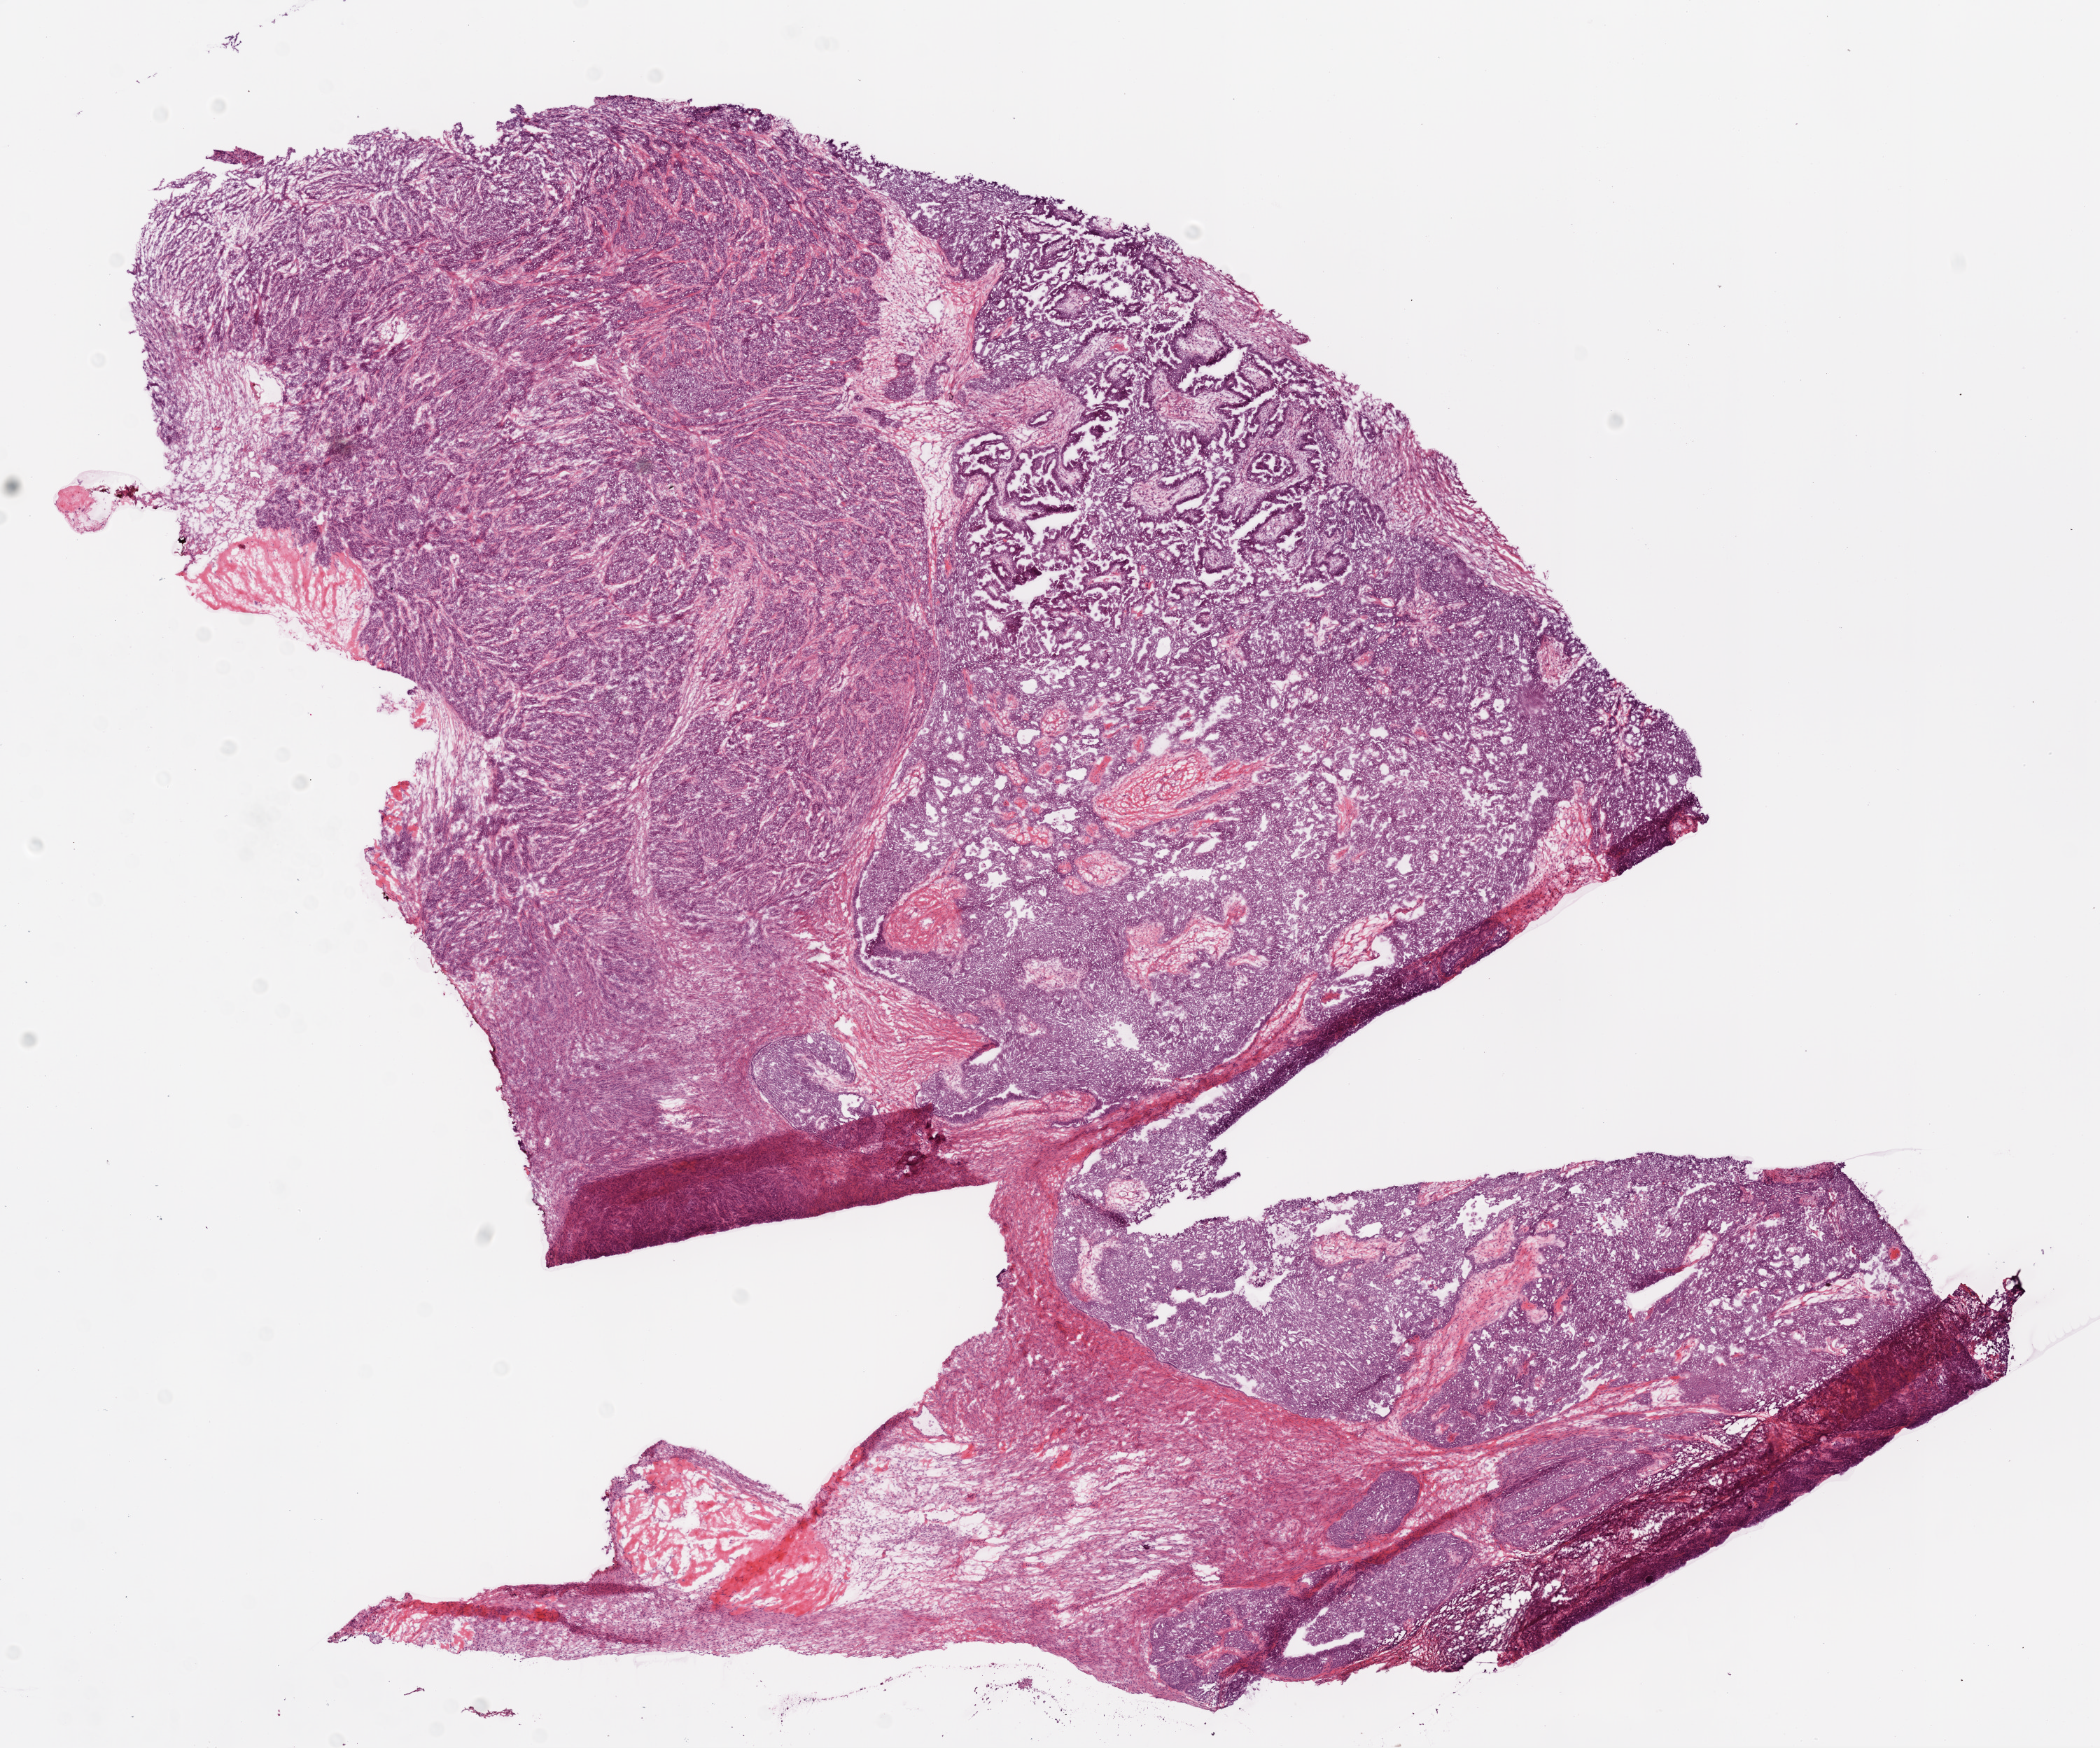
Whole-slide histology image, Hematoxylin and eosin (H&E) stained, a low-resolution overview of the entire scanned area, about 12.0 x 10.0 mm (slide scanned at 20x). Frozen section from the top of the tissue portion. Sample: primary tumour, ovary. Patient: female, age at initial diagnosis 51 years. Histologic grade: G3 (poorly differentiated). Composition of this section per pathologist review: tumour cells 90%, tumour nuclei 90%, normal cells 0%, stromal cells 10%, necrosis 0%.
• diagnosis: Serous cystadenocarcinoma, NOS
• FIGO stage: IIIC